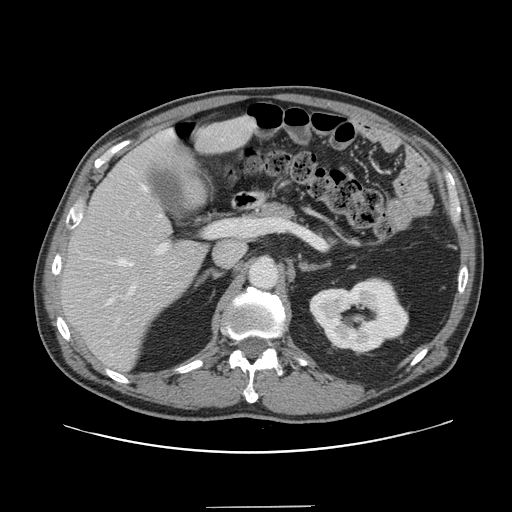
Contrast-enhanced abdominal CT, one axial slice; position 85 of 139 along the scan axis; 120 kVp; intravenous contrast given; soft-tissue window (W 400 / L 40 HU); 2.5 mm slice thickness; 512 × 512 image matrix, field of view 397 × 397 mm. Male patient, age 64 years. Case-level facts recorded for this patient, not image findings: diagnosis: colorectal cancer liver metastases, imaged before liver resection.
Outlined on this slice (expert manual segmentation):
- hepatic veins: box from (x=107, y=186) to (x=162, y=305) px
- liver: (x=62, y=118)–(x=254, y=369)
- planned liver remnant (the part of the liver to remain after resection): (x=62, y=118)–(x=253, y=369)
- portal vein (with intrahepatic branches): (x=118, y=224)–(x=218, y=321)